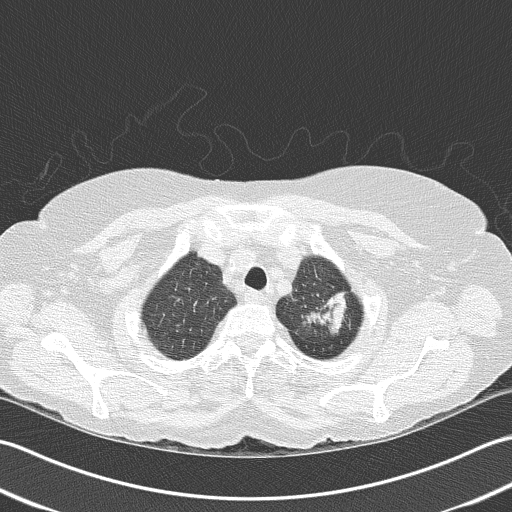
Axial slice from a low-dose chest CT screening exam, first (baseline) screen, lung window (W 1500 / L -600 HU), 2 mm slice thickness, 512 × 512 image matrix. Female, age 68 years at enrolment. Former smoker at enrolment.
- Lesion marked by an expert reader, bounding box [x1, y1, x2, y2] px = [290, 271, 363, 339].
- No non-calcified nodule or mass ≥4 mm was recorded by the screening reader at this exam.
- Official screen result: negative screen, minor abnormalities not suspicious for lung cancer.
- Participant outcome: lung cancer diagnosed 763 days after this screen (after the third annual screen) — adenocarcinoma, NOS, left upper lobe, poorly differentiated (G3), stage IB (AJCC 6th edition), 50 mm at pathology.